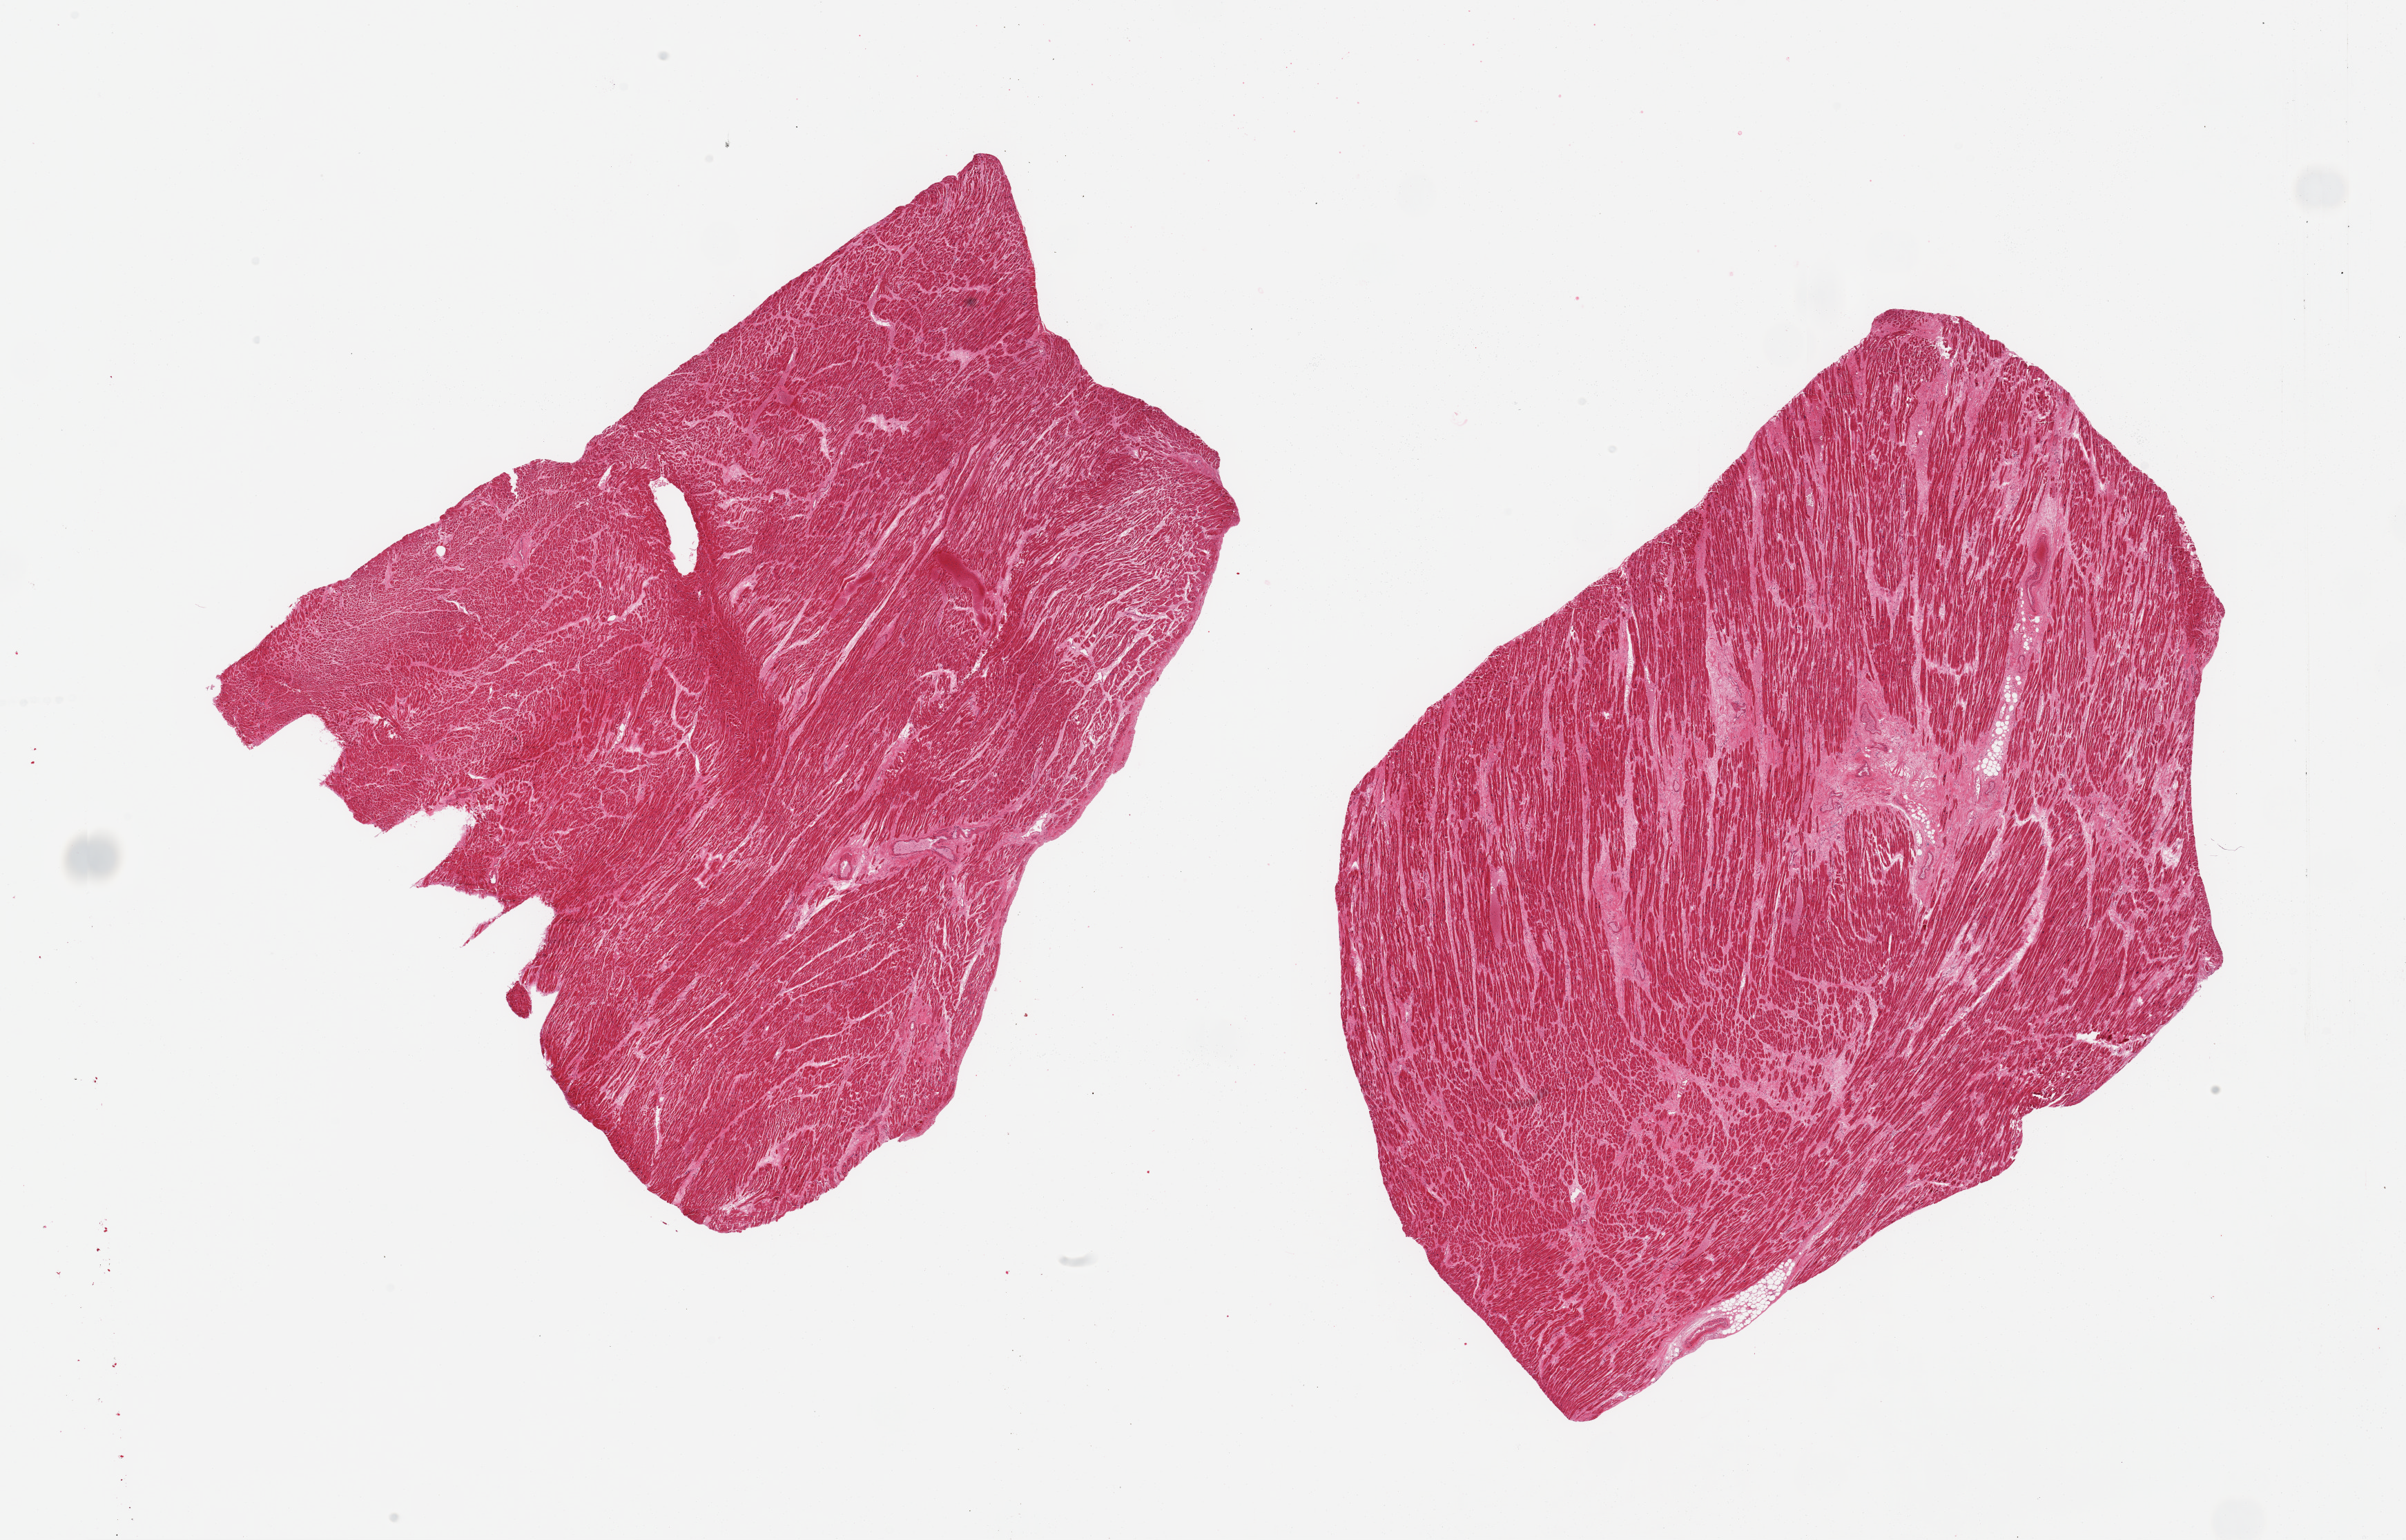
Whole-slide image, H&E stain, shown as a low-resolution overview of the whole scanned area (about 27.6 x 17.6 mm, slide scanned at 20x), PAXgene-fixed paraffin-embedded (PFPE) section, section of heart (target tissue), donor tissue sample. Male donor.
* review note (as recorded): 2 pieces, advanced interstitial fibrosis/chronic ischemic changes with remote 2mm infarct